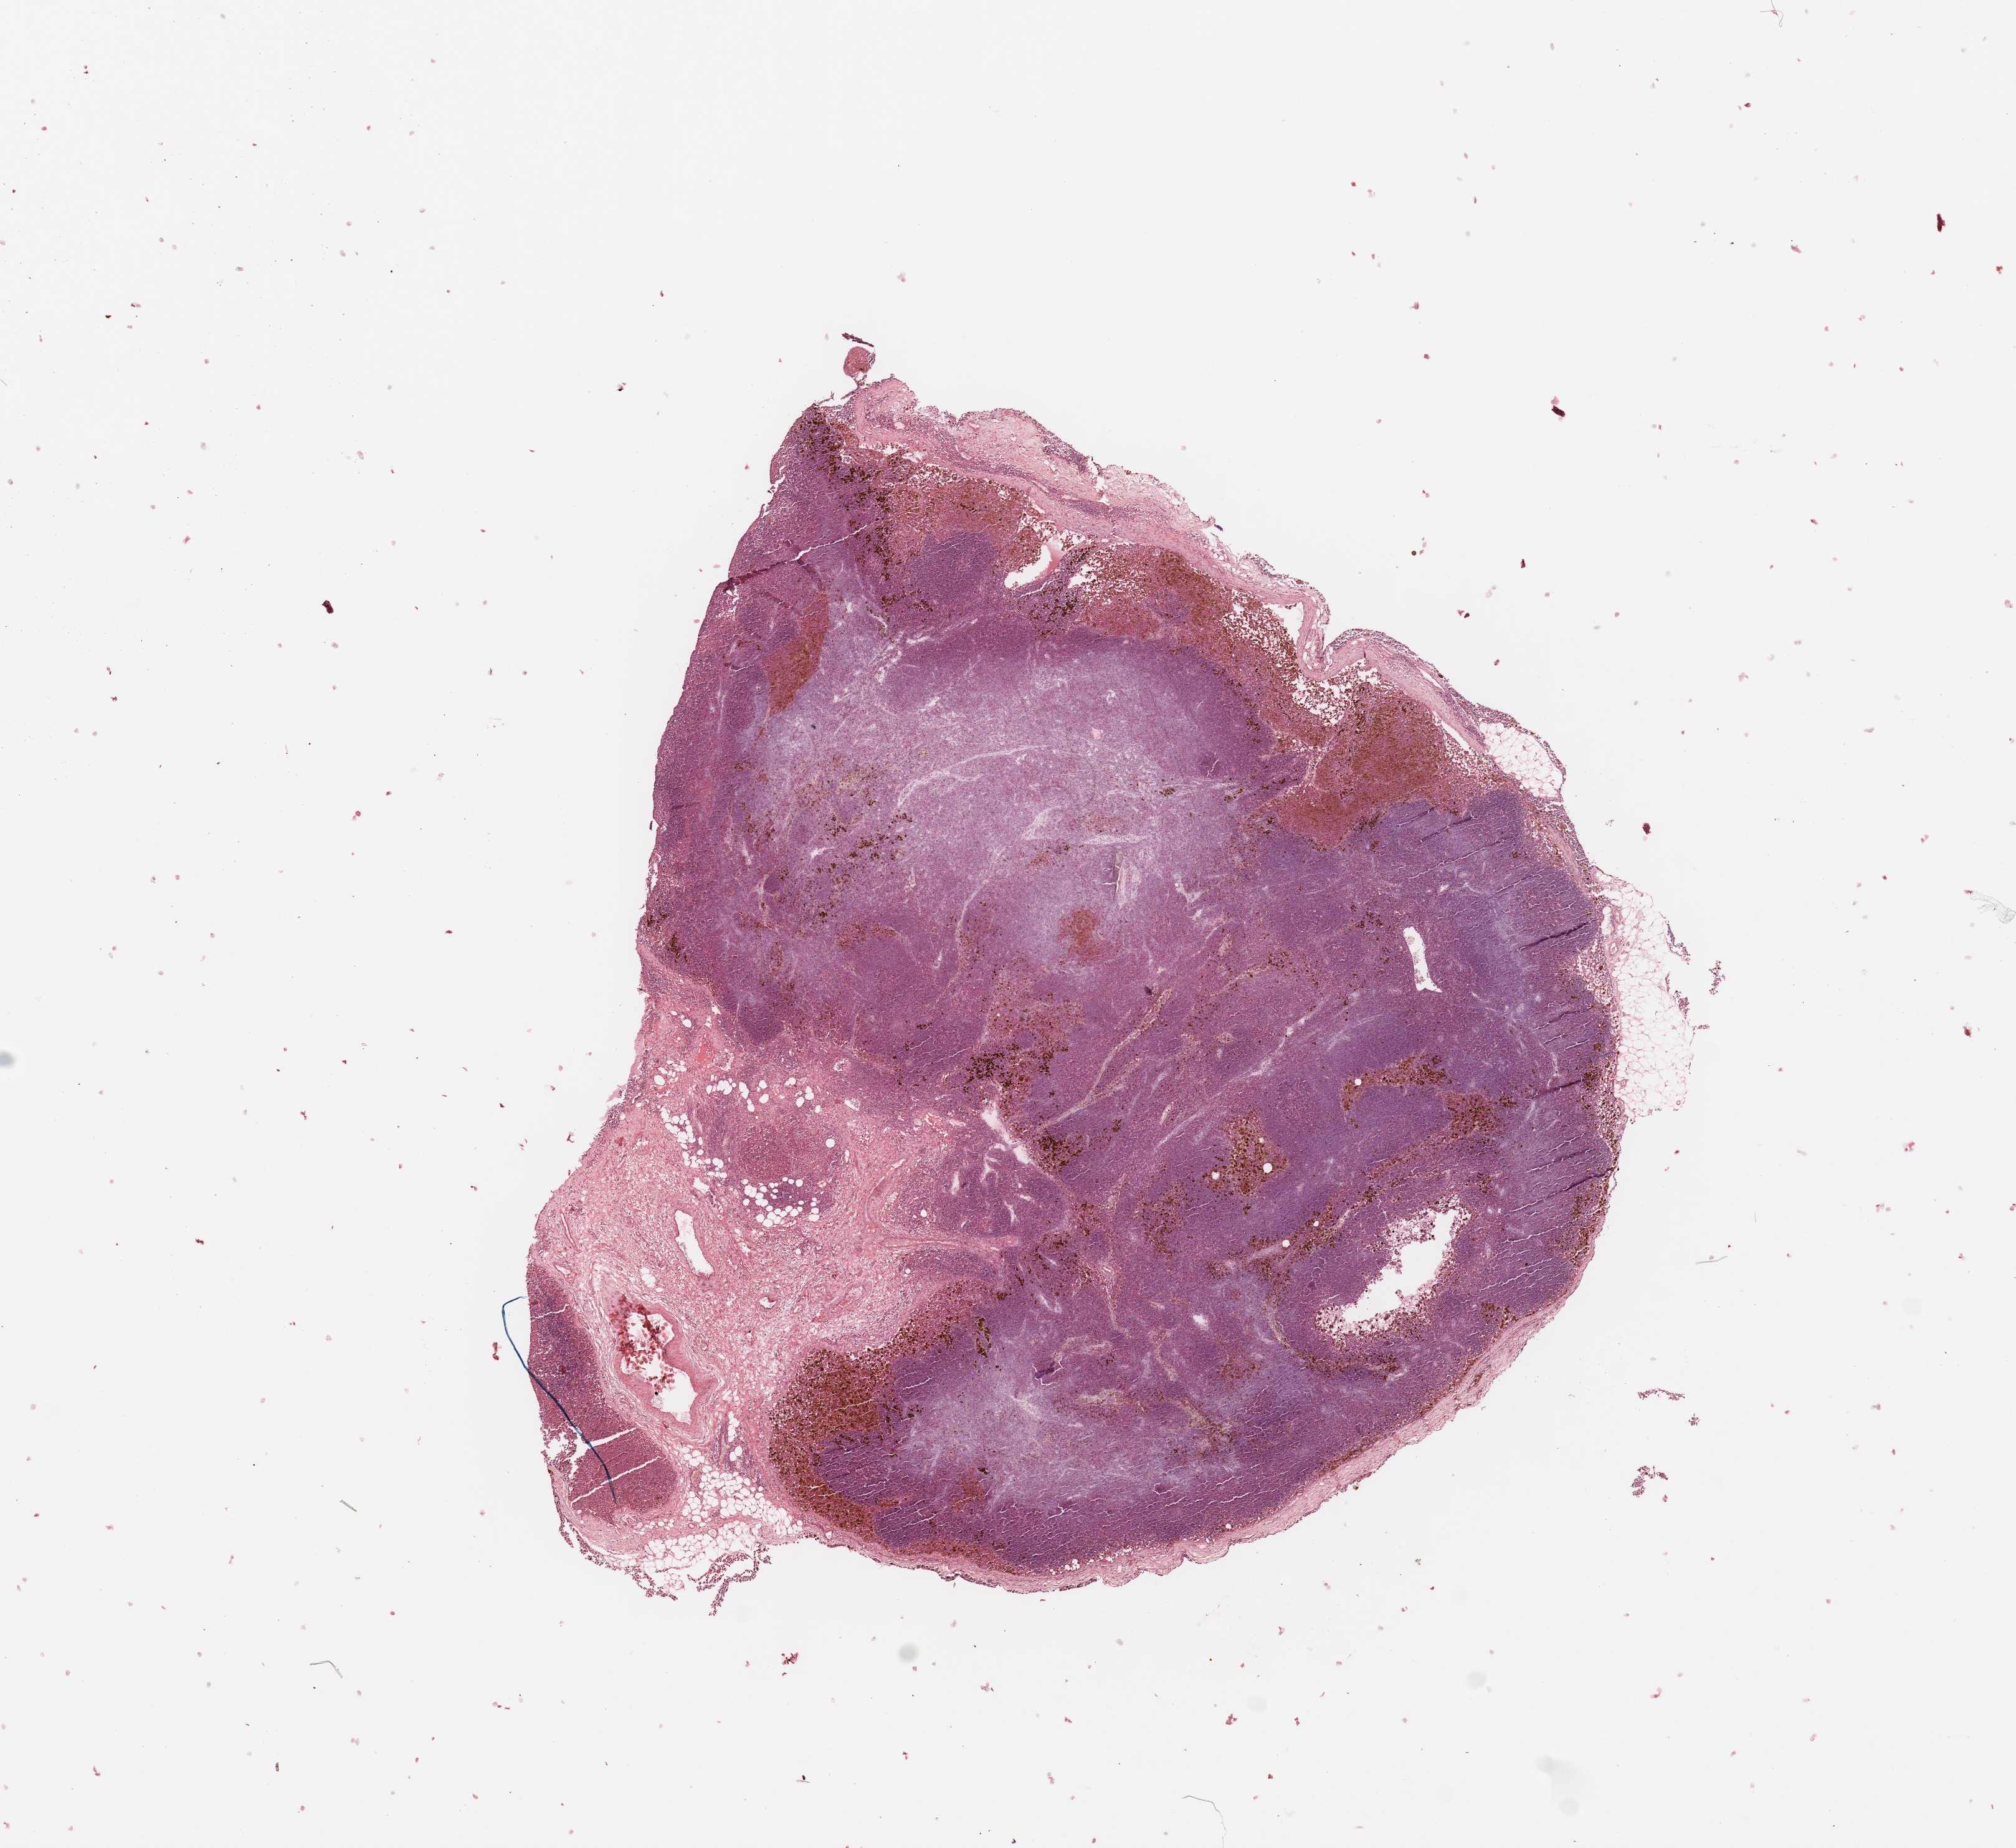
H&E-stained whole-slide image — whole scanned area (about 12.8 x 11.7 mm, acquisition: 20x scan) shown as a low-resolution overview; melanoma tumour tissue; sampled site not recorded. Female, 44 y/o.
Primary tumour site (as recorded): trunk. Patient diagnosis (cohort enrolment): cutaneous melanoma (skin).